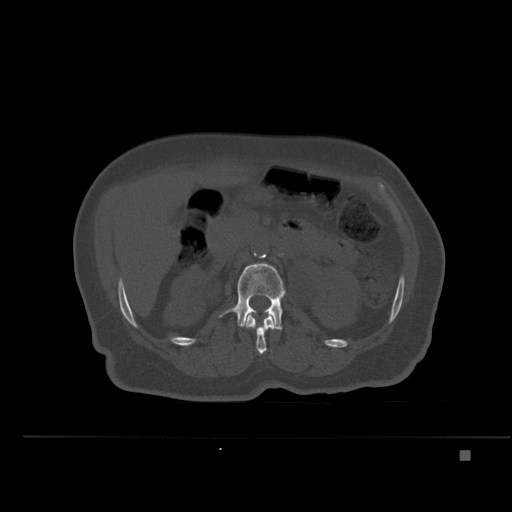
CT including the spine, one axial slice; position 223 of 477 along the scan axis; bone window (W 1800 / L 400 HU); 1.5 mm slice thickness; 512 × 512 image matrix, field of view 422 × 422 mm. Patient: female, 74 years. Case-level facts recorded for this patient, not image findings: primary cancer: colon.
Outlined on this slice (semi-automatically segmented with operator editing):
- L1 vertebra: box from (x=244, y=312) to (x=276, y=354) px
- L2 vertebra: (x=221, y=263)–(x=286, y=330)